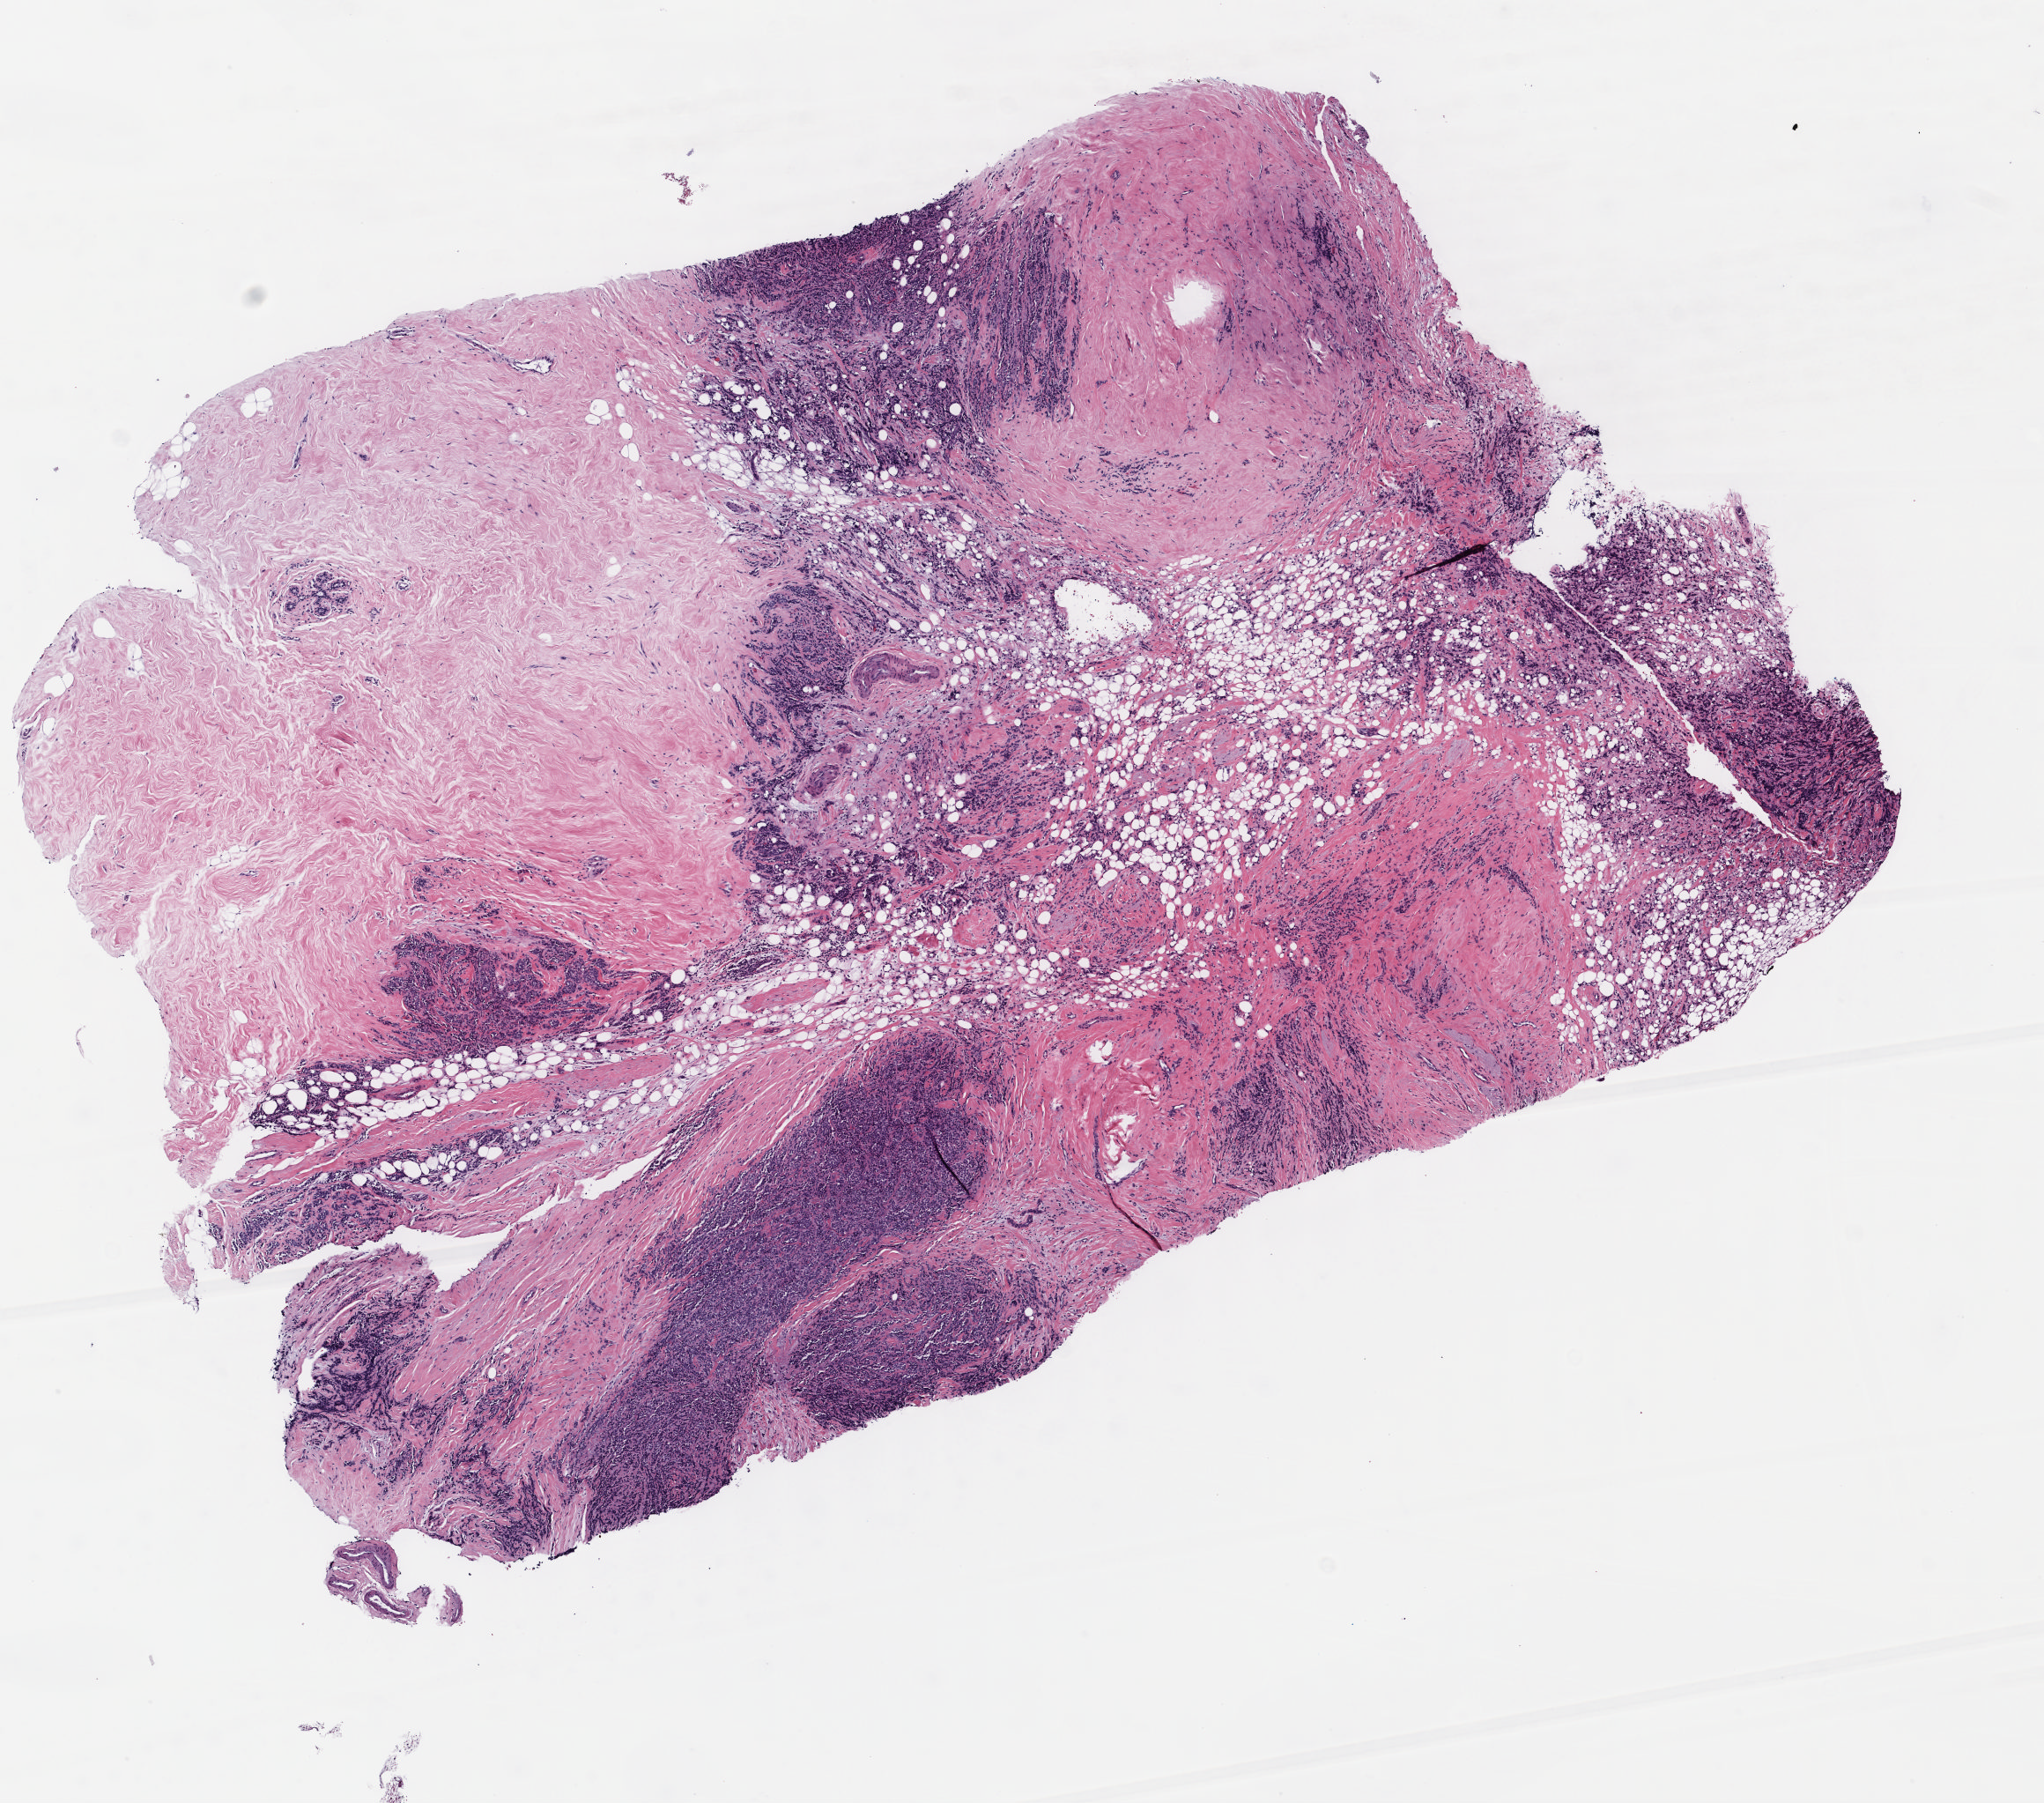
Hematoxylin and eosin (H&E) stained whole-slide image — whole scanned area (about 9.1 x 8.0 mm) shown as a low-resolution overview. Formalin-fixed paraffin-embedded (FFPE) diagnostic section. Primary tumour sample from the breast. Female patient; age at initial diagnosis 62 years.
AJCC pathologic stage: IIA. Lymph nodes positive (case pathology): 1 of 1 examined. Diagnosis: Lobular carcinoma, NOS.